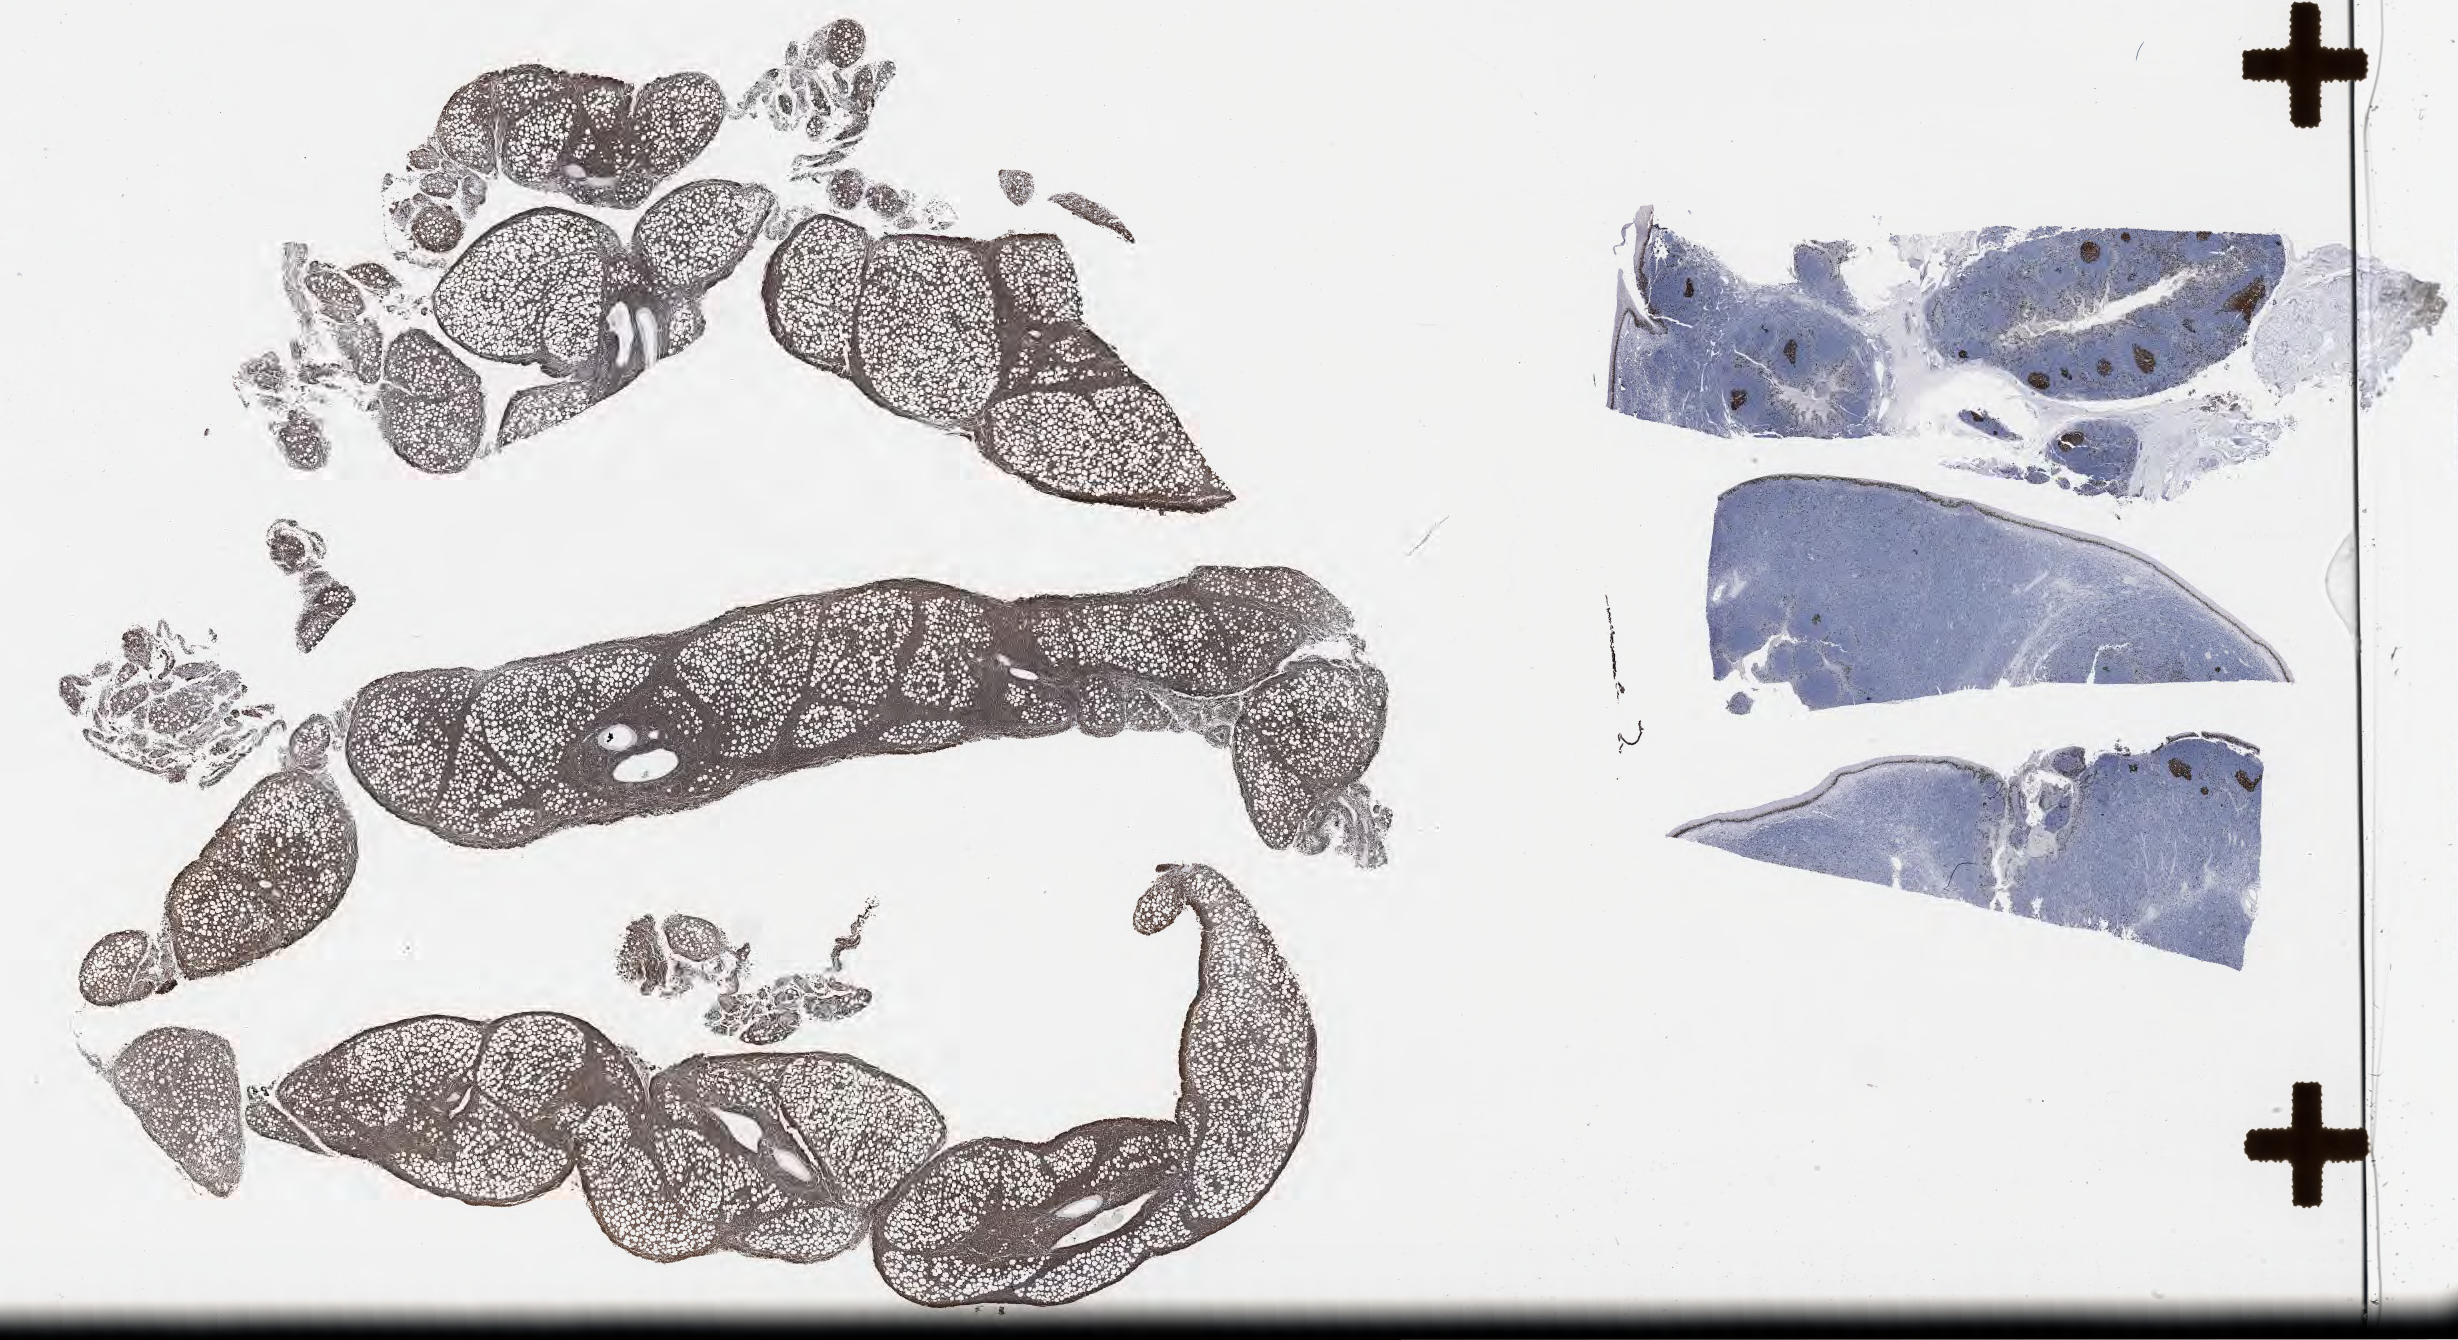
IHC for Ki-67, whole-slide image — low-resolution overview of the scanned area, about 39.8 x 21.7 mm, tumor tissue, anatomic site: abdomen proper. Female, age 9 years at initial diagnosis.
Histologic diagnosis: Burkitt lymphoma, NOS.